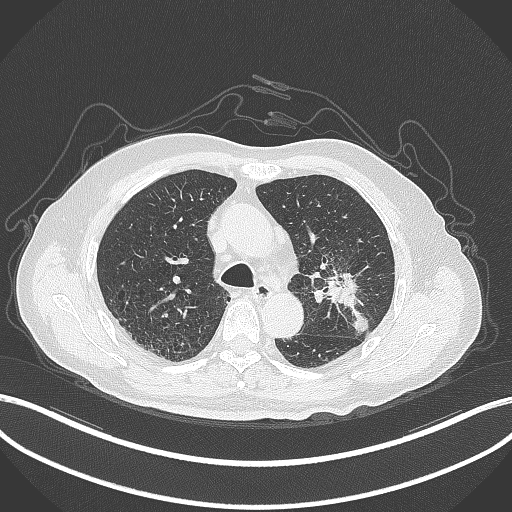
Chest CT, one axial slice. Slice 194 of 331 in the series (ordered by position). Lung window (W 1500 / L -600 HU). 512 × 512 image matrix, field of view 400 × 400 mm. Male patient, age 79 years. Case-level facts recorded for this patient, not image findings: clinical TNM (as recorded): T2a N1 M1.
Annotated regions visible in this slice (bounding box drawn by a radiologist):
- lung tumour (recorded histology: adenocarcinoma): bounding box <318,271,374,338> (left, top, right, bottom; pixels)